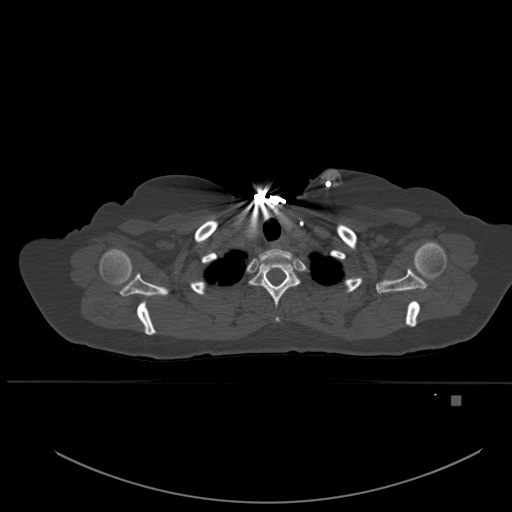
CT including the spine, one axial slice; slice 419 of 651 in the series (ordered by position); bone window (W 1800 / L 400 HU); 1.5 mm slice thickness; 512 × 512 image matrix, field of view 443 × 443 mm. Female patient, age 49 years. From the clinical record (not read from this slice): primary cancer: breast; vertebrae with lytic lesions (as recorded): L3, T12, L4.
Outlined on this slice (semi-automatic segmentation, software-assisted and operator-edited):
- T1 vertebra: bounding box (x1, y1, x2, y2) in pixels: (249, 259, 300, 322)